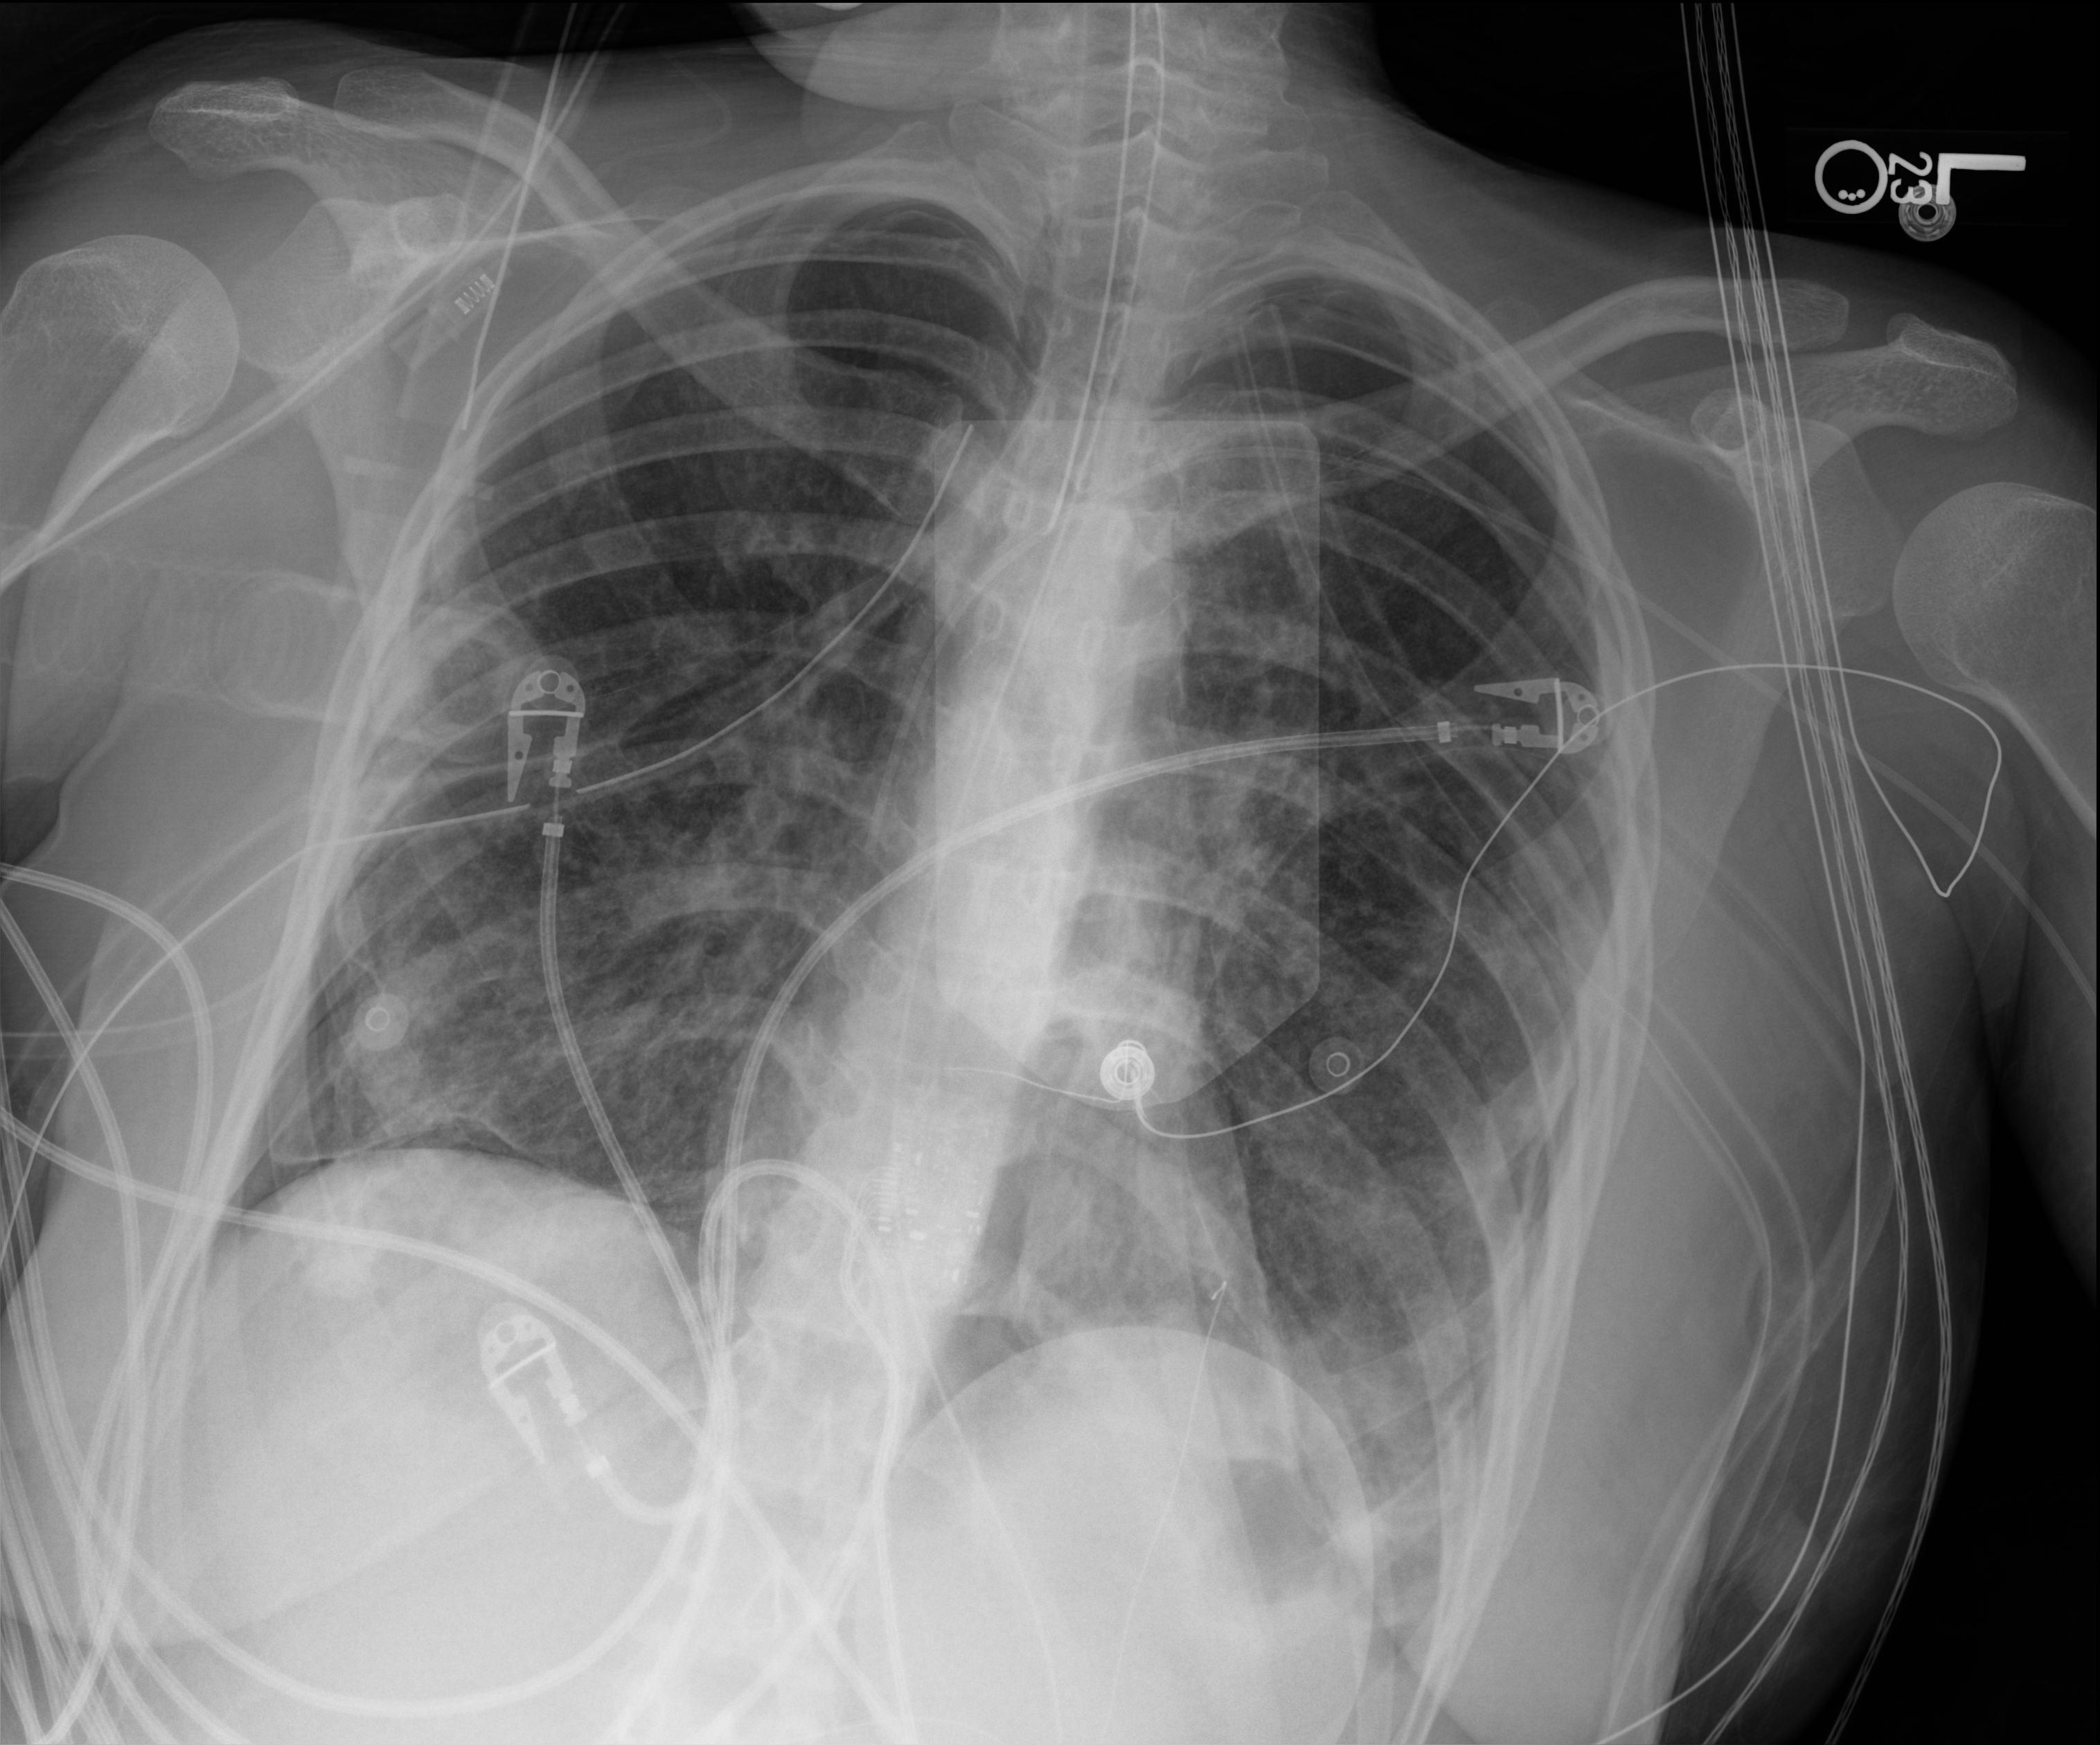
Bedside chest radiograph (digital radiography), anteroposterior (AP) projection. Adult patient hospitalised with COVID-19, age 18–59 years.
Hospital-stay facts (about this admission, not read from this image; timing relative to this image not recorded): COPD (admission record): no; smoking status (admission record): never; admitted to intensive care during this hospital stay: yes.